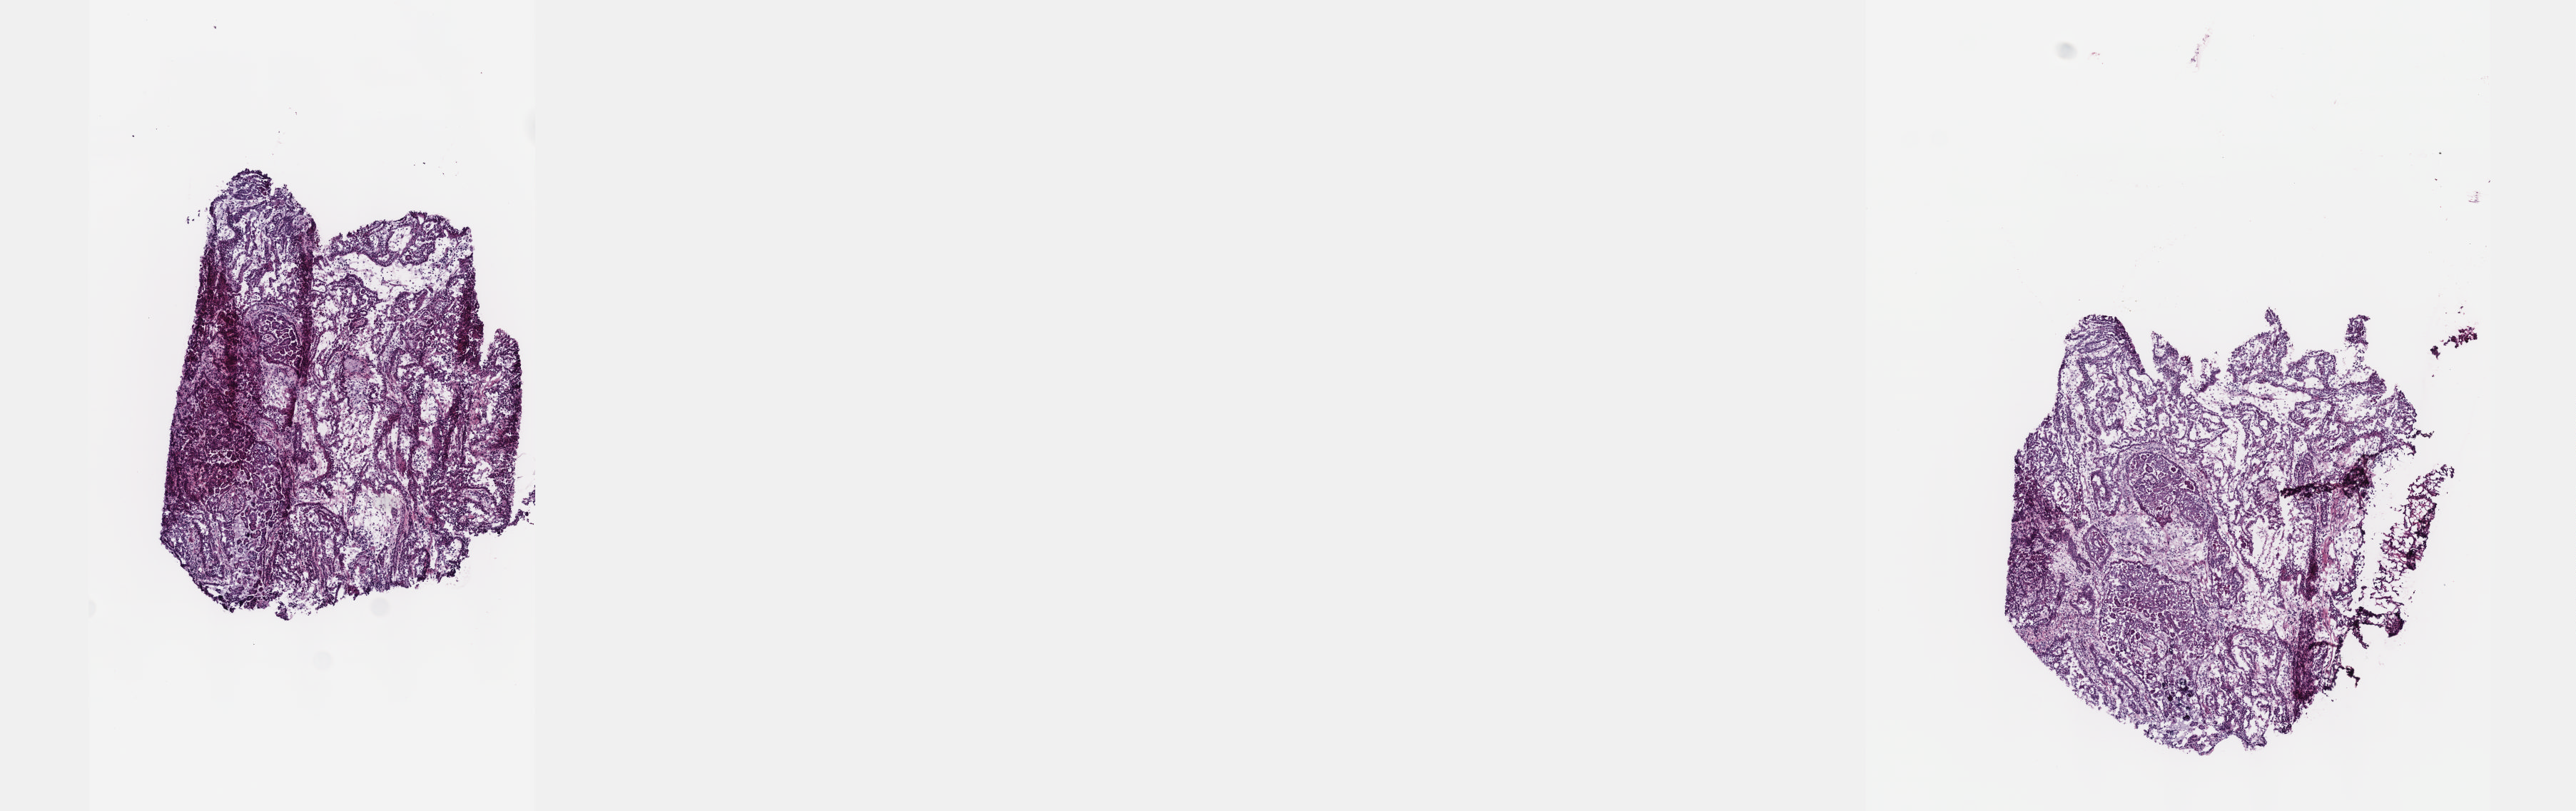
Hematoxylin and eosin (H&E) stained whole-slide image, shown as a low-resolution overview of the whole scanned area (about 14.6 x 4.6 mm, slide scanned at 40x), frozen section from the top of the tissue portion, kidney, primary tumour sample. Male patient; age at initial diagnosis 71 years. Pathologist review of this section (percent, as recorded): tumour cells 70%, tumour nuclei 65%, normal cells 0%, stromal cells 28%, necrosis 2%. Inflammatory infiltration, as recorded: lymphocyte infiltration 20%, monocyte infiltration 8%, neutrophil infiltration 3%.
Laterality: left. Diagnosis: Papillary adenocarcinoma, NOS. AJCC pathologic stage: III (7th edition). Lymph nodes positive (case pathology): 14 of 20 examined.